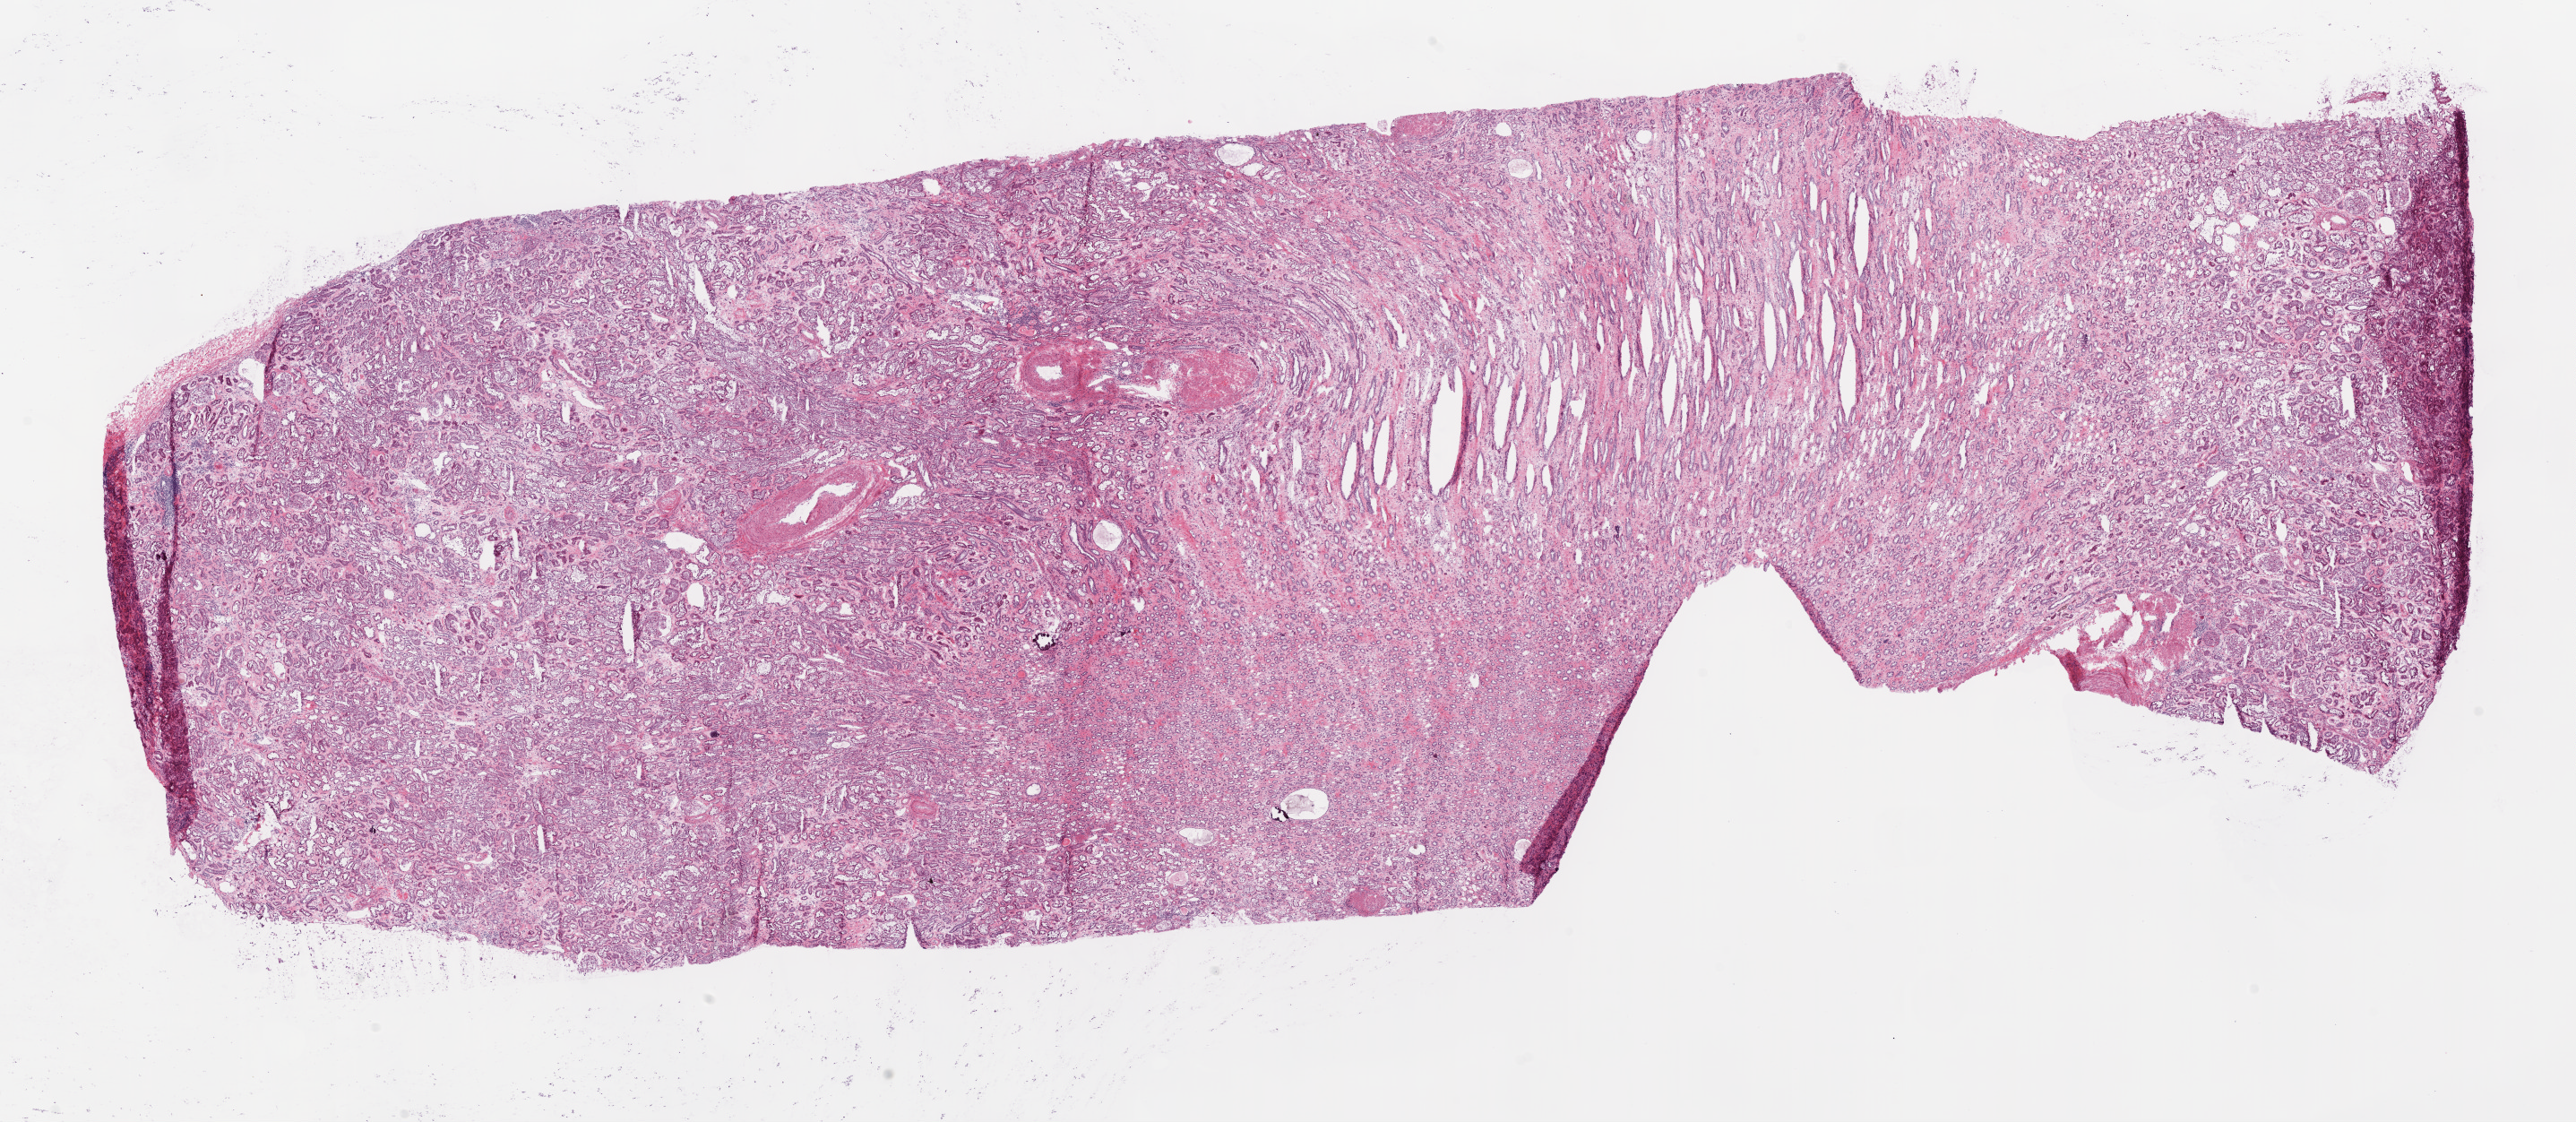
Digitized H&E tissue section (whole slide), low-resolution overview of the scanned area, about 23.1 x 10.0 mm; frozen section from the bottom of the tissue portion; sample: solid tissue normal (non-tumour tissue), kidney. Male, age 73 years at initial diagnosis.
This section: solid tissue normal sample (biorepository sample class). Patient diagnosis: Clear cell adenocarcinoma, NOS.